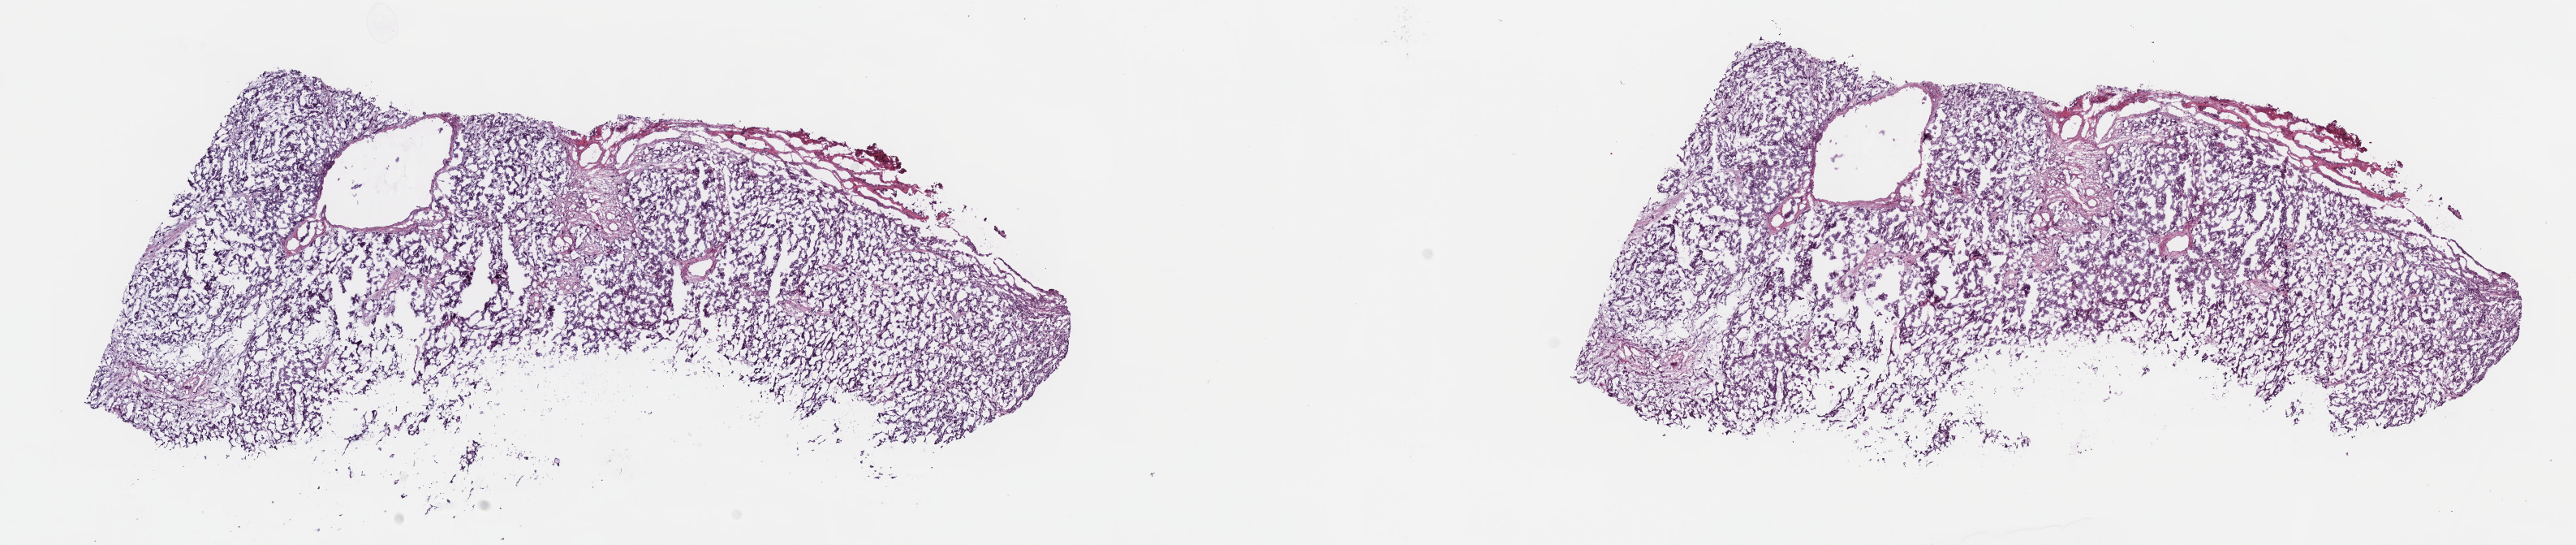
H&E whole-slide image — whole scanned area (about 25.7 x 5.4 mm, from a 40x scan) shown as a low-resolution overview, frozen section from the top of the tissue portion, liver, primary tumour sample. Patient: female, age at initial diagnosis 81 years. Histologic grade: G4 (undifferentiated). Composition of this section per pathologist review: tumour cells 95%, tumour nuclei 85%, normal cells 0%, stromal cells 5%, necrosis 0%. Inflammatory infiltration, as recorded: lymphocyte infiltration 0%, monocyte infiltration 0%, neutrophil infiltration 0%.
AJCC pathologic stage: I (6th edition). Pathologic diagnosis: Combined hepatocellular carcinoma and cholangiocarcinoma.